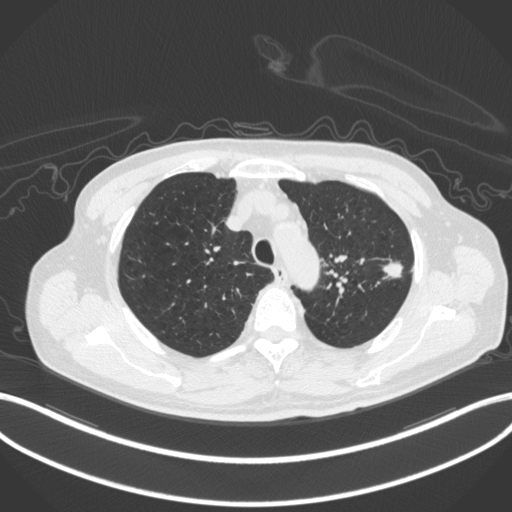
Chest CT, one axial slice; slice 347 of 420 in the series (ordered by position); reconstruction kernel B31f; 120 kVp; lung window (W 1500 / L -600 HU); 1 mm slice thickness; 512 × 512 image matrix. Male patient, age 77 years. Case-level facts recorded for this patient, not image findings: clinical TNM (as recorded): T3 N1 M0.
Outlined on this slice (bounding box drawn by a radiologist):
- lung tumour (recorded histology: adenocarcinoma): bounding box (x1, y1, x2, y2) in pixels: (380, 256, 404, 281)